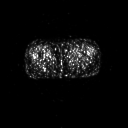
FDG PET of an extremity soft-tissue mass (from a PET/CT study), one axial slice; position 1 of 267 along the scan axis; 3.27 mm slice thickness; 128 × 128 image matrix, field of view 700 × 700 mm. Patient: female, 47 years. From the clinical record (not read from this slice): histological type: myxofibrosarcoma; grade: intermediate; site of the primary tumour: left thigh.
Structures marked on this image (expert contour drawn on MRI and transferred to this co-registered scan by the dataset authors):
- gross tumour volume including surrounding oedema: bounding box (x1, y1, x2, y2) in pixels: (70, 55, 80, 59)